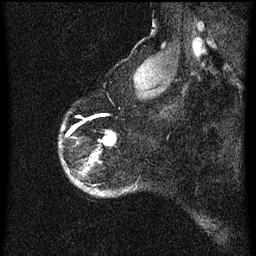
Breast MRI (dynamic contrast-enhanced), one sagittal slice; position 53 of 60 along the scan axis; dynamic contrast-enhanced series, image 2 of 3 at this slice position (ordered by acquisition); 1.5 T; TE 4.2 ms, TR 8 ms; 2 mm slice thickness; 256 × 256 image matrix, field of view 180 × 180 mm. Patient: female, 56 years.
Structures marked on this image (semi-automatically segmented with operator editing):
- analysis volume of interest (the breast-tissue region the enhancement analysis was run in; not a lesion): box from (x=64, y=130) to (x=117, y=197) px
- tumour enhancement mask (voxels above the 70 % enhancement threshold inside the analysis volume of interest): (x=86, y=136)–(x=115, y=171)